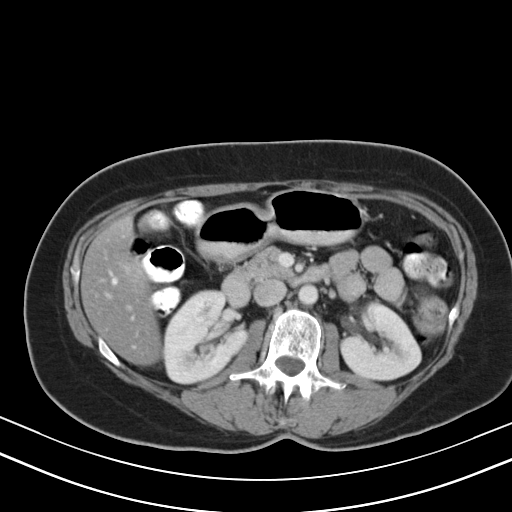
Contrast-enhanced abdominal CT, one axial slice; position 21 of 47 along the scan axis; reconstruction kernel B40s; 130 kVp; soft-tissue window (W 400 / L 40 HU); 5 mm slice thickness; 512 × 512 image matrix, field of view 350 × 350 mm. Female patient. Case-level facts recorded for this patient, not image findings: diagnosis: colorectal cancer liver metastases, imaged before liver resection; multiple liver metastases: no; largest metastasis: 3.5 cm; disease in both lobes: no.
Annotated regions visible in this slice (manually delineated by an expert):
- hepatic veins: bounding box <112,278,116,283> (left, top, right, bottom; pixels)
- liver: <82,221,160,362>
- planned liver remnant (the part of the liver to remain after resection): <82,221,160,362>
- portal vein (with intrahepatic branches): <128,262,148,282>